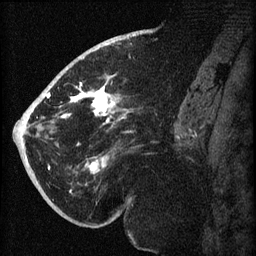
Breast MRI (dynamic contrast-enhanced), one sagittal slice. Dynamic contrast-enhanced series, image 2 of 3 at this slice position (ordered by acquisition). 1.5 T. TE 4.2 ms, TR 8.2 ms. 256 × 256 image matrix, field of view 180 × 180 mm. Patient: female, 71 years.
Annotated regions visible in this slice (semi-automatic segmentation, software-assisted and operator-edited):
- analysis volume of interest (the breast-tissue region the enhancement analysis was run in; not a lesion): box from (x=40, y=72) to (x=142, y=196) px
- tumour enhancement mask (voxels above the 70 % enhancement threshold inside the analysis volume of interest): (x=44, y=82)–(x=125, y=193)